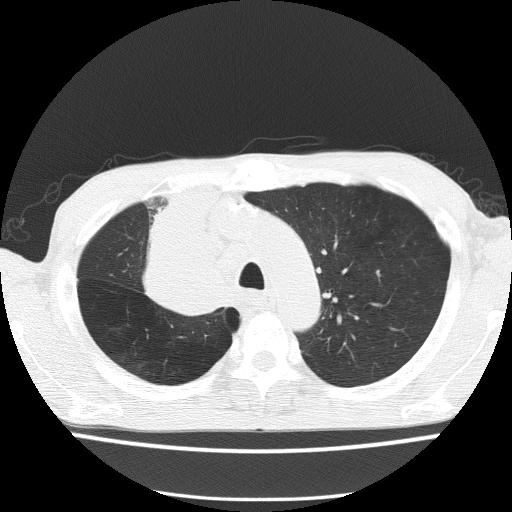
Low-dose screening chest CT, axial slice, baseline screening round, lung window (W 1500 / L -600 HU), 2 mm slice thickness, 512 × 512 image matrix, field of view 336 × 336 mm. Male participant, aged 59 years at enrolment. Former smoker at enrolment.
Expert reader's lesion annotation, bounding box [x1, y1, x2, y2] px = [132, 234, 238, 326]. The screening reader recorded 5 non-calcified nodules or masses ≥4 mm on this exam; which of them this box marks is not recorded. Participant outcome: lung cancer diagnosed 72 days after this screen — squamous cell carcinoma, NOS, right upper lobe, moderately differentiated (G2), stage IV (AJCC 6th edition).